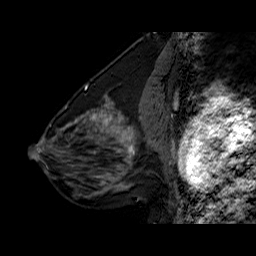
Breast MRI (dynamic contrast-enhanced), one sagittal slice. Slice 27 of 60 in the series (ordered by position). Dynamic contrast-enhanced series, time point 2 of 6 at this slice position (early post-contrast). 1.5 T. TE 6.3 ms, TR 32.5 ms. 256 × 256 image matrix, field of view 200 × 200 mm. Female patient. From the clinical record (not read from this slice): setting: breast cancer imaged before/during neoadjuvant chemotherapy; receptor status: triple-negative.
Structures marked on this image (semi-automatic segmentation, software-assisted and operator-edited):
- analysis volume of interest (the breast-tissue region the enhancement analysis was run in; not a lesion): box from (x=108, y=126) to (x=154, y=177) px
- tumour enhancement mask (voxels above the 100 % enhancement threshold inside the analysis volume of interest): (x=116, y=128)–(x=135, y=159)